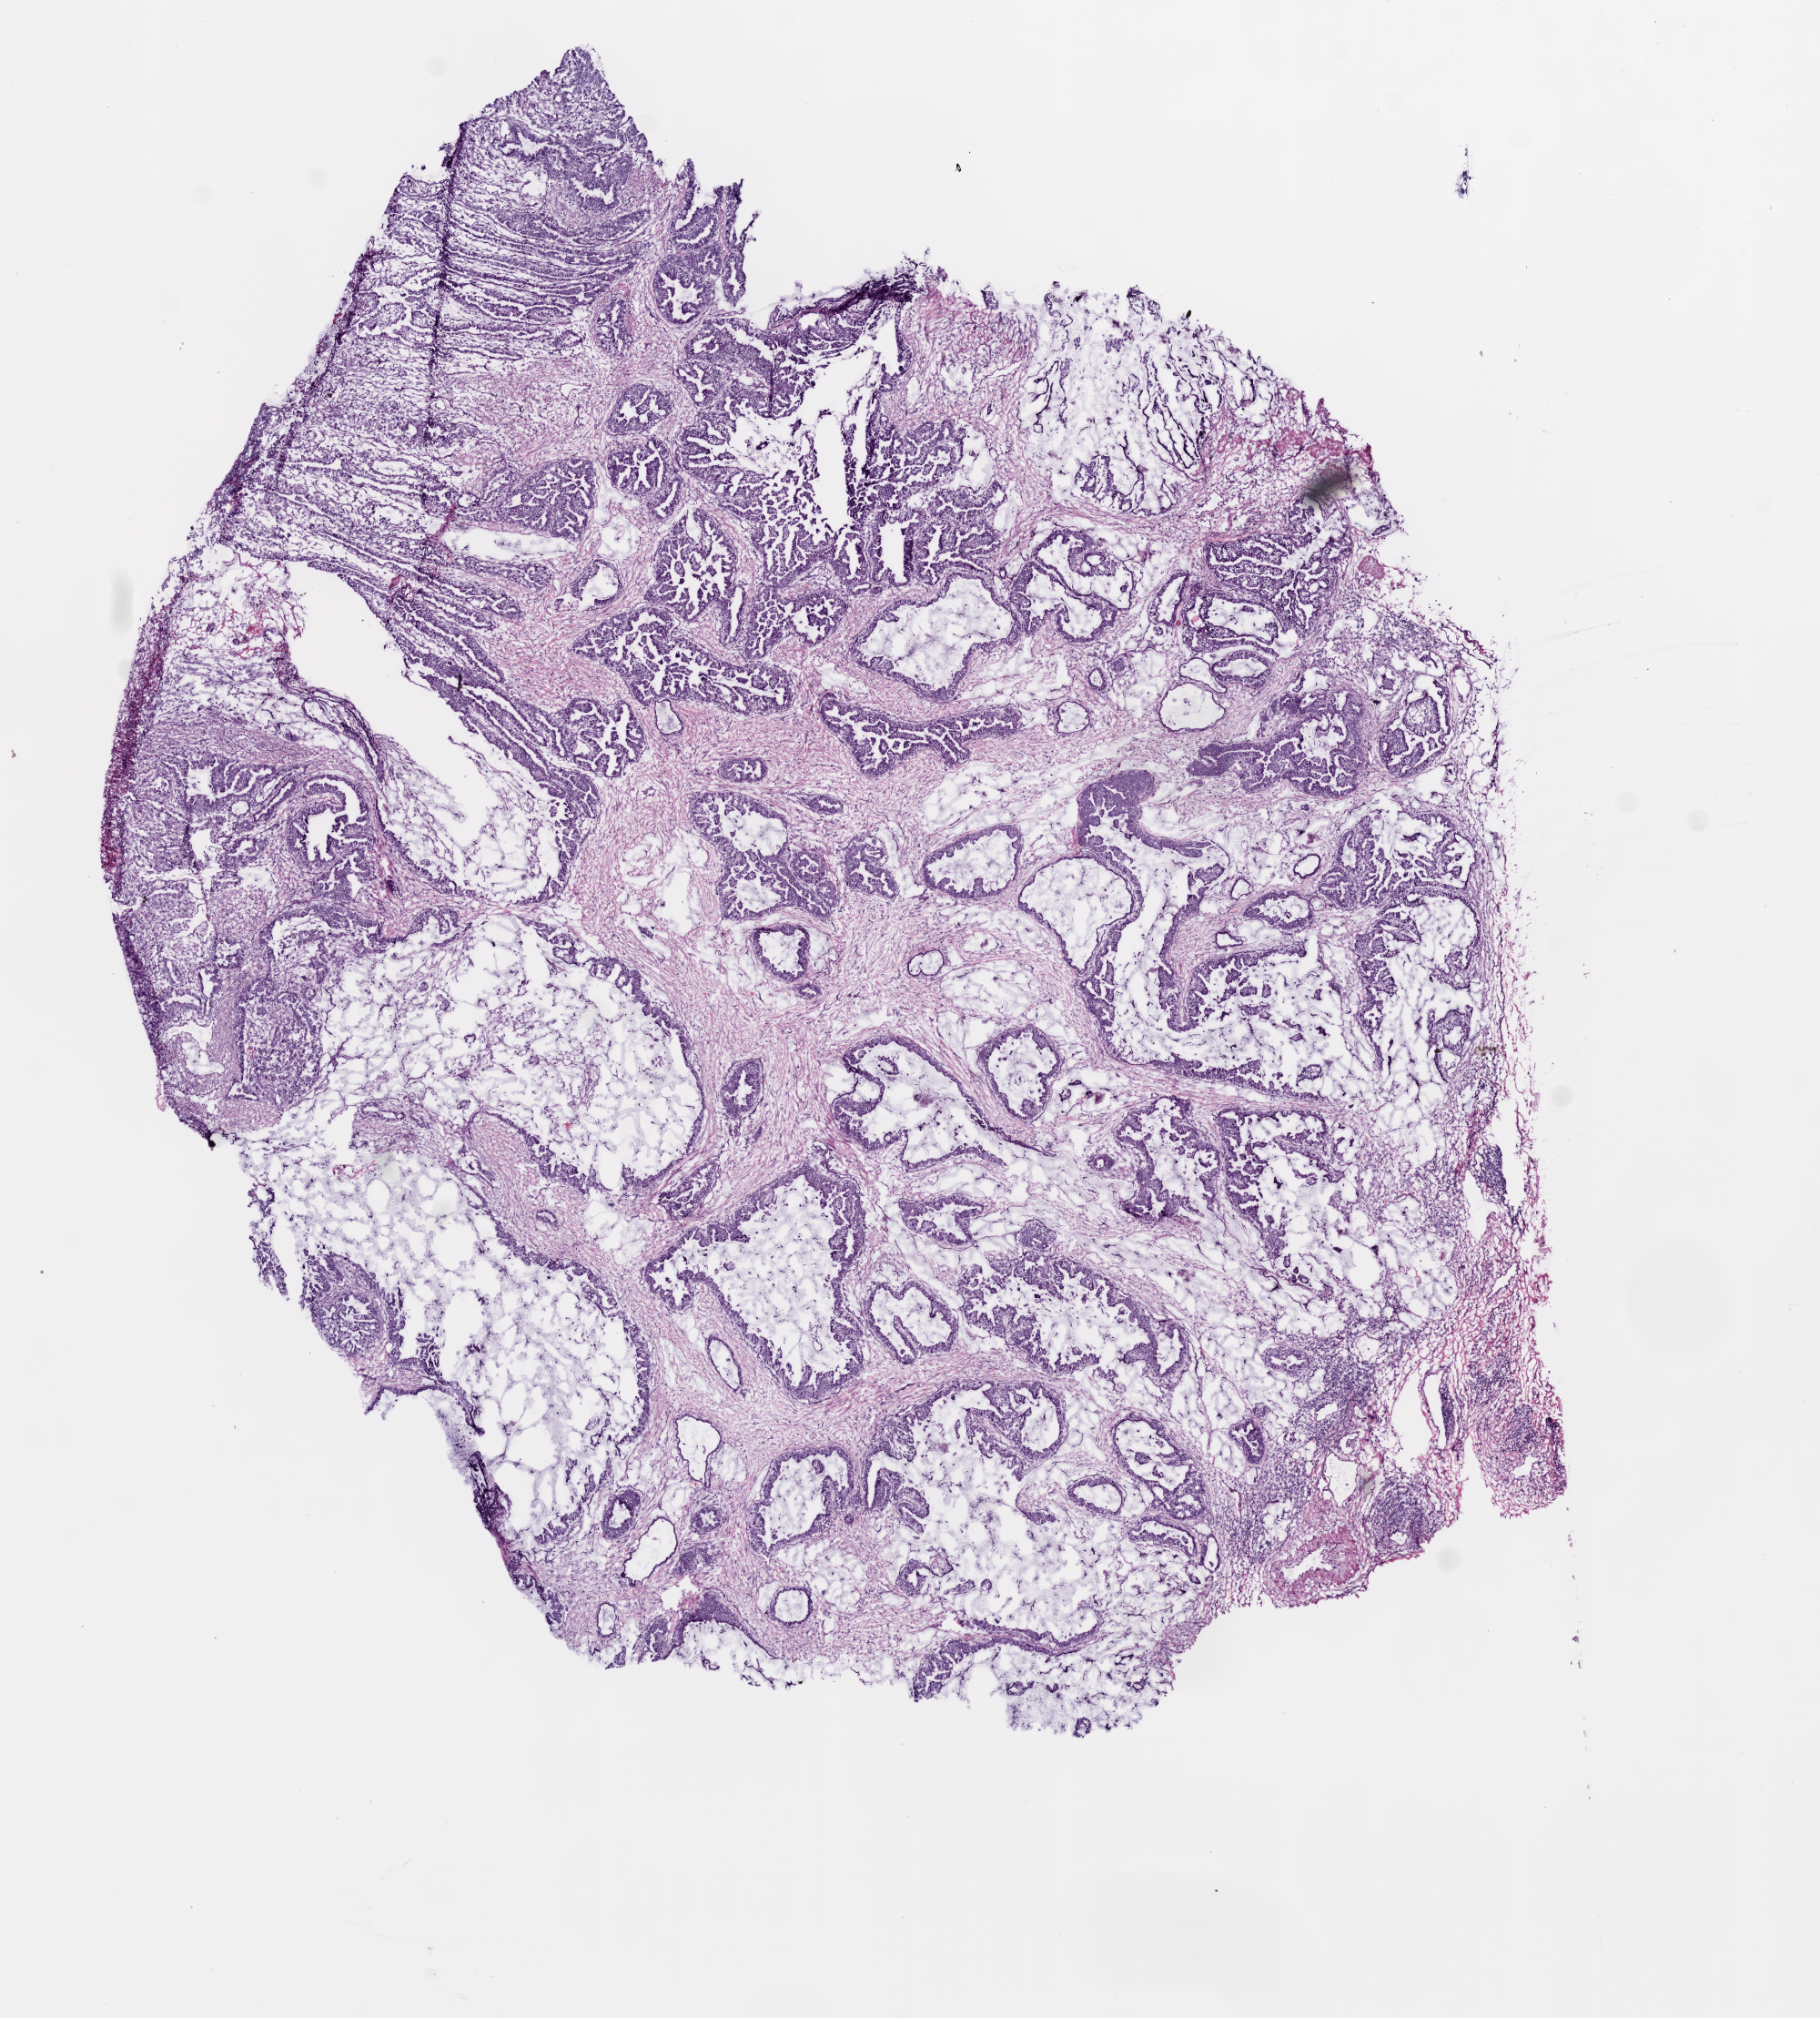
Digitized H&E-stained tissue section (whole slide), shown as a low-resolution overview of the whole scanned area (about 8.0 x 8.9 mm, slide scanned at 20x). Frozen section from the bottom of the tissue portion. Stomach, primary tumour sample. Patient: male, age at initial diagnosis 81 years. Histologic grade: G2 (moderately differentiated). Composition of this section per pathologist review: tumour cells 60%, tumour nuclei 75%, normal cells 5%, stromal cells 30%, necrosis 5%.
AJCC pathologic stage: II (5th edition). Histologic diagnosis: Mucinous adenocarcinoma. Lymph nodes positive (case pathology): 6 of 42 examined.